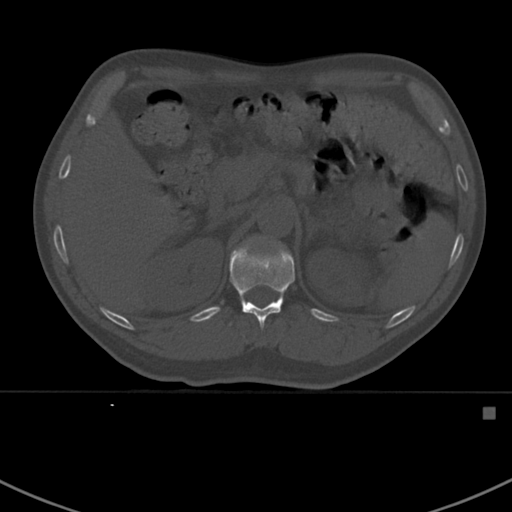
CT including the spine, one axial slice. Slice 327 of 412 in the series (ordered by position). Reconstruction kernel Br40s. 120 kVp. Bone window (W 1800 / L 400 HU). 1.5 mm slice thickness. 512 × 512 image matrix, field of view 358 × 358 mm. Male patient, age 59 years. From the clinical record (not read from this slice): primary cancer: prostate.
Annotated regions visible in this slice (semi-automatic segmentation, software-assisted and operator-edited):
- T12 vertebra: bounding box (x1, y1, x2, y2) in pixels: (230, 243, 295, 330)